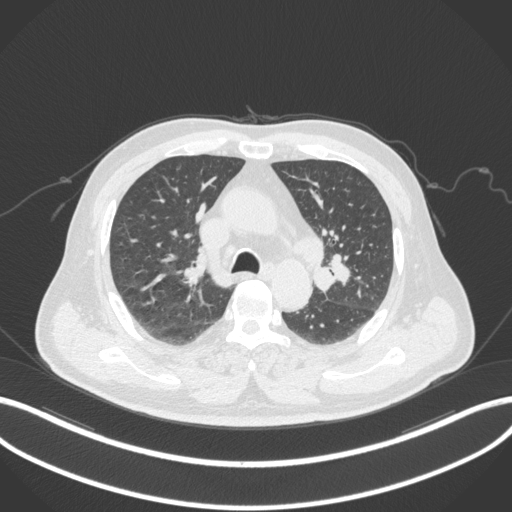
Chest CT, one axial slice. Slice 200 of 286 in the series (ordered by position). Reconstruction kernel B31f. 120 kVp. Lung window (W 1500 / L -600 HU). 512 × 512 image matrix. Patient: male, 67 years. Case-level facts recorded for this patient, not image findings: clinical TNM (as recorded): T2a N1 M0.
Outlined on this slice (bounding box drawn by a radiologist):
- lung tumour (recorded histology: adenocarcinoma): bounding box <311,251,355,295> (left, top, right, bottom; pixels)